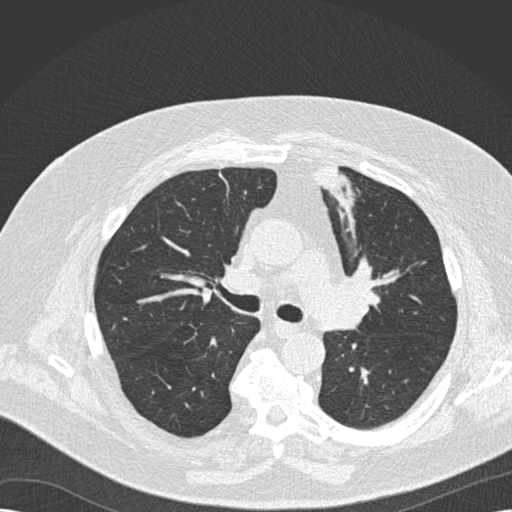
Low-dose screening chest CT, one axial slice. 120 kVp. Lung window (W 1500 / L -600 HU). 512 × 512 image matrix.
Annotated regions visible in this slice (manually delineated by an expert):
- lesion 1 (tumor, upper lobe of left lung): bounding box [x1, y1, x2, y2] px = [316, 166, 354, 205]